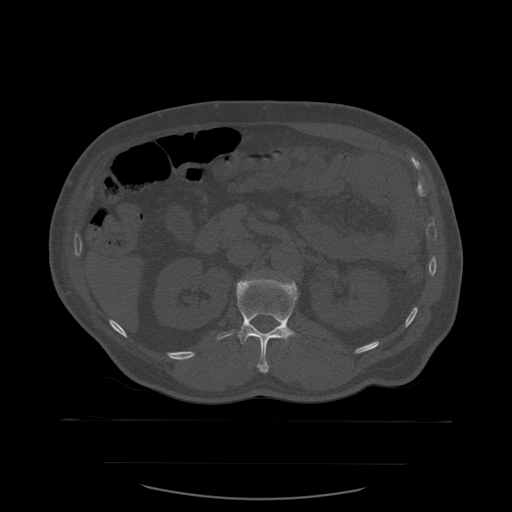
CT including the spine, one axial slice. Position 245 of 590 along the scan axis. Bone window (W 1800 / L 400 HU). 1.25 mm slice thickness. 512 × 512 image matrix, field of view 479 × 479 mm. Patient age 71 years. Case-level facts recorded for this patient, not image findings: primary cancer: lung.
Structures marked on this image (semi-automatically segmented with operator editing):
- L1 vertebra: box from (x=216, y=276) to (x=298, y=373) px